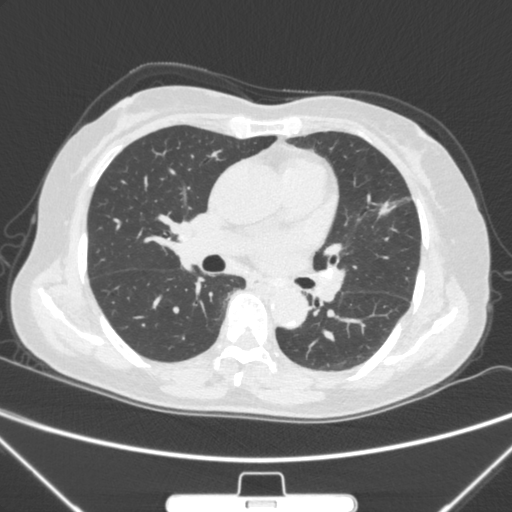
Chest CT, one axial slice; slice 152 of 300 in the series (ordered by position); 120 kVp; lung window (W 1500 / L -600 HU); 1 mm slice thickness; 512 × 512 image matrix, field of view 350 × 350 mm. Female patient, age 70 years. Case-level facts recorded for this patient, not image findings: clinical TNM (as recorded): T1b N0 M0; histopathological grade: G2.
Structures marked on this image (rectangle marked by the reading radiologist):
- lung tumour (recorded histology: adenocarcinoma): box from (x=373, y=194) to (x=397, y=222) px